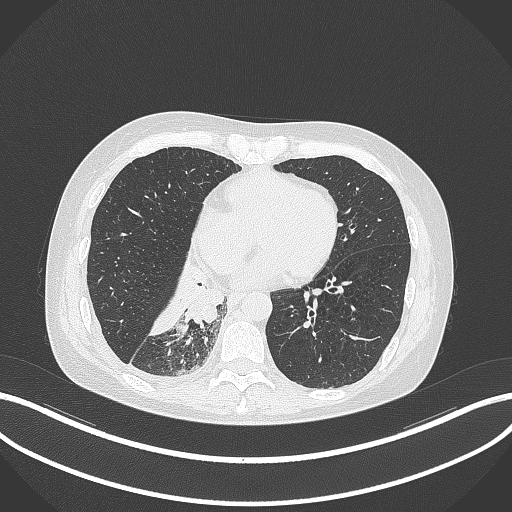
Chest CT, one axial slice. Position 111 of 329 along the scan axis. Reconstruction kernel B70f. 120 kVp. Lung window (W 1500 / L -600 HU). 1 mm slice thickness. 512 × 512 image matrix. Patient: female, 63 years. From the clinical record (not read from this slice): clinical TNM (as recorded): T1c N0 M0.
Annotated regions visible in this slice (bounding box drawn by a radiologist):
- lung tumour (recorded histology: adenocarcinoma): bounding box [x1, y1, x2, y2] px = [177, 280, 225, 324]